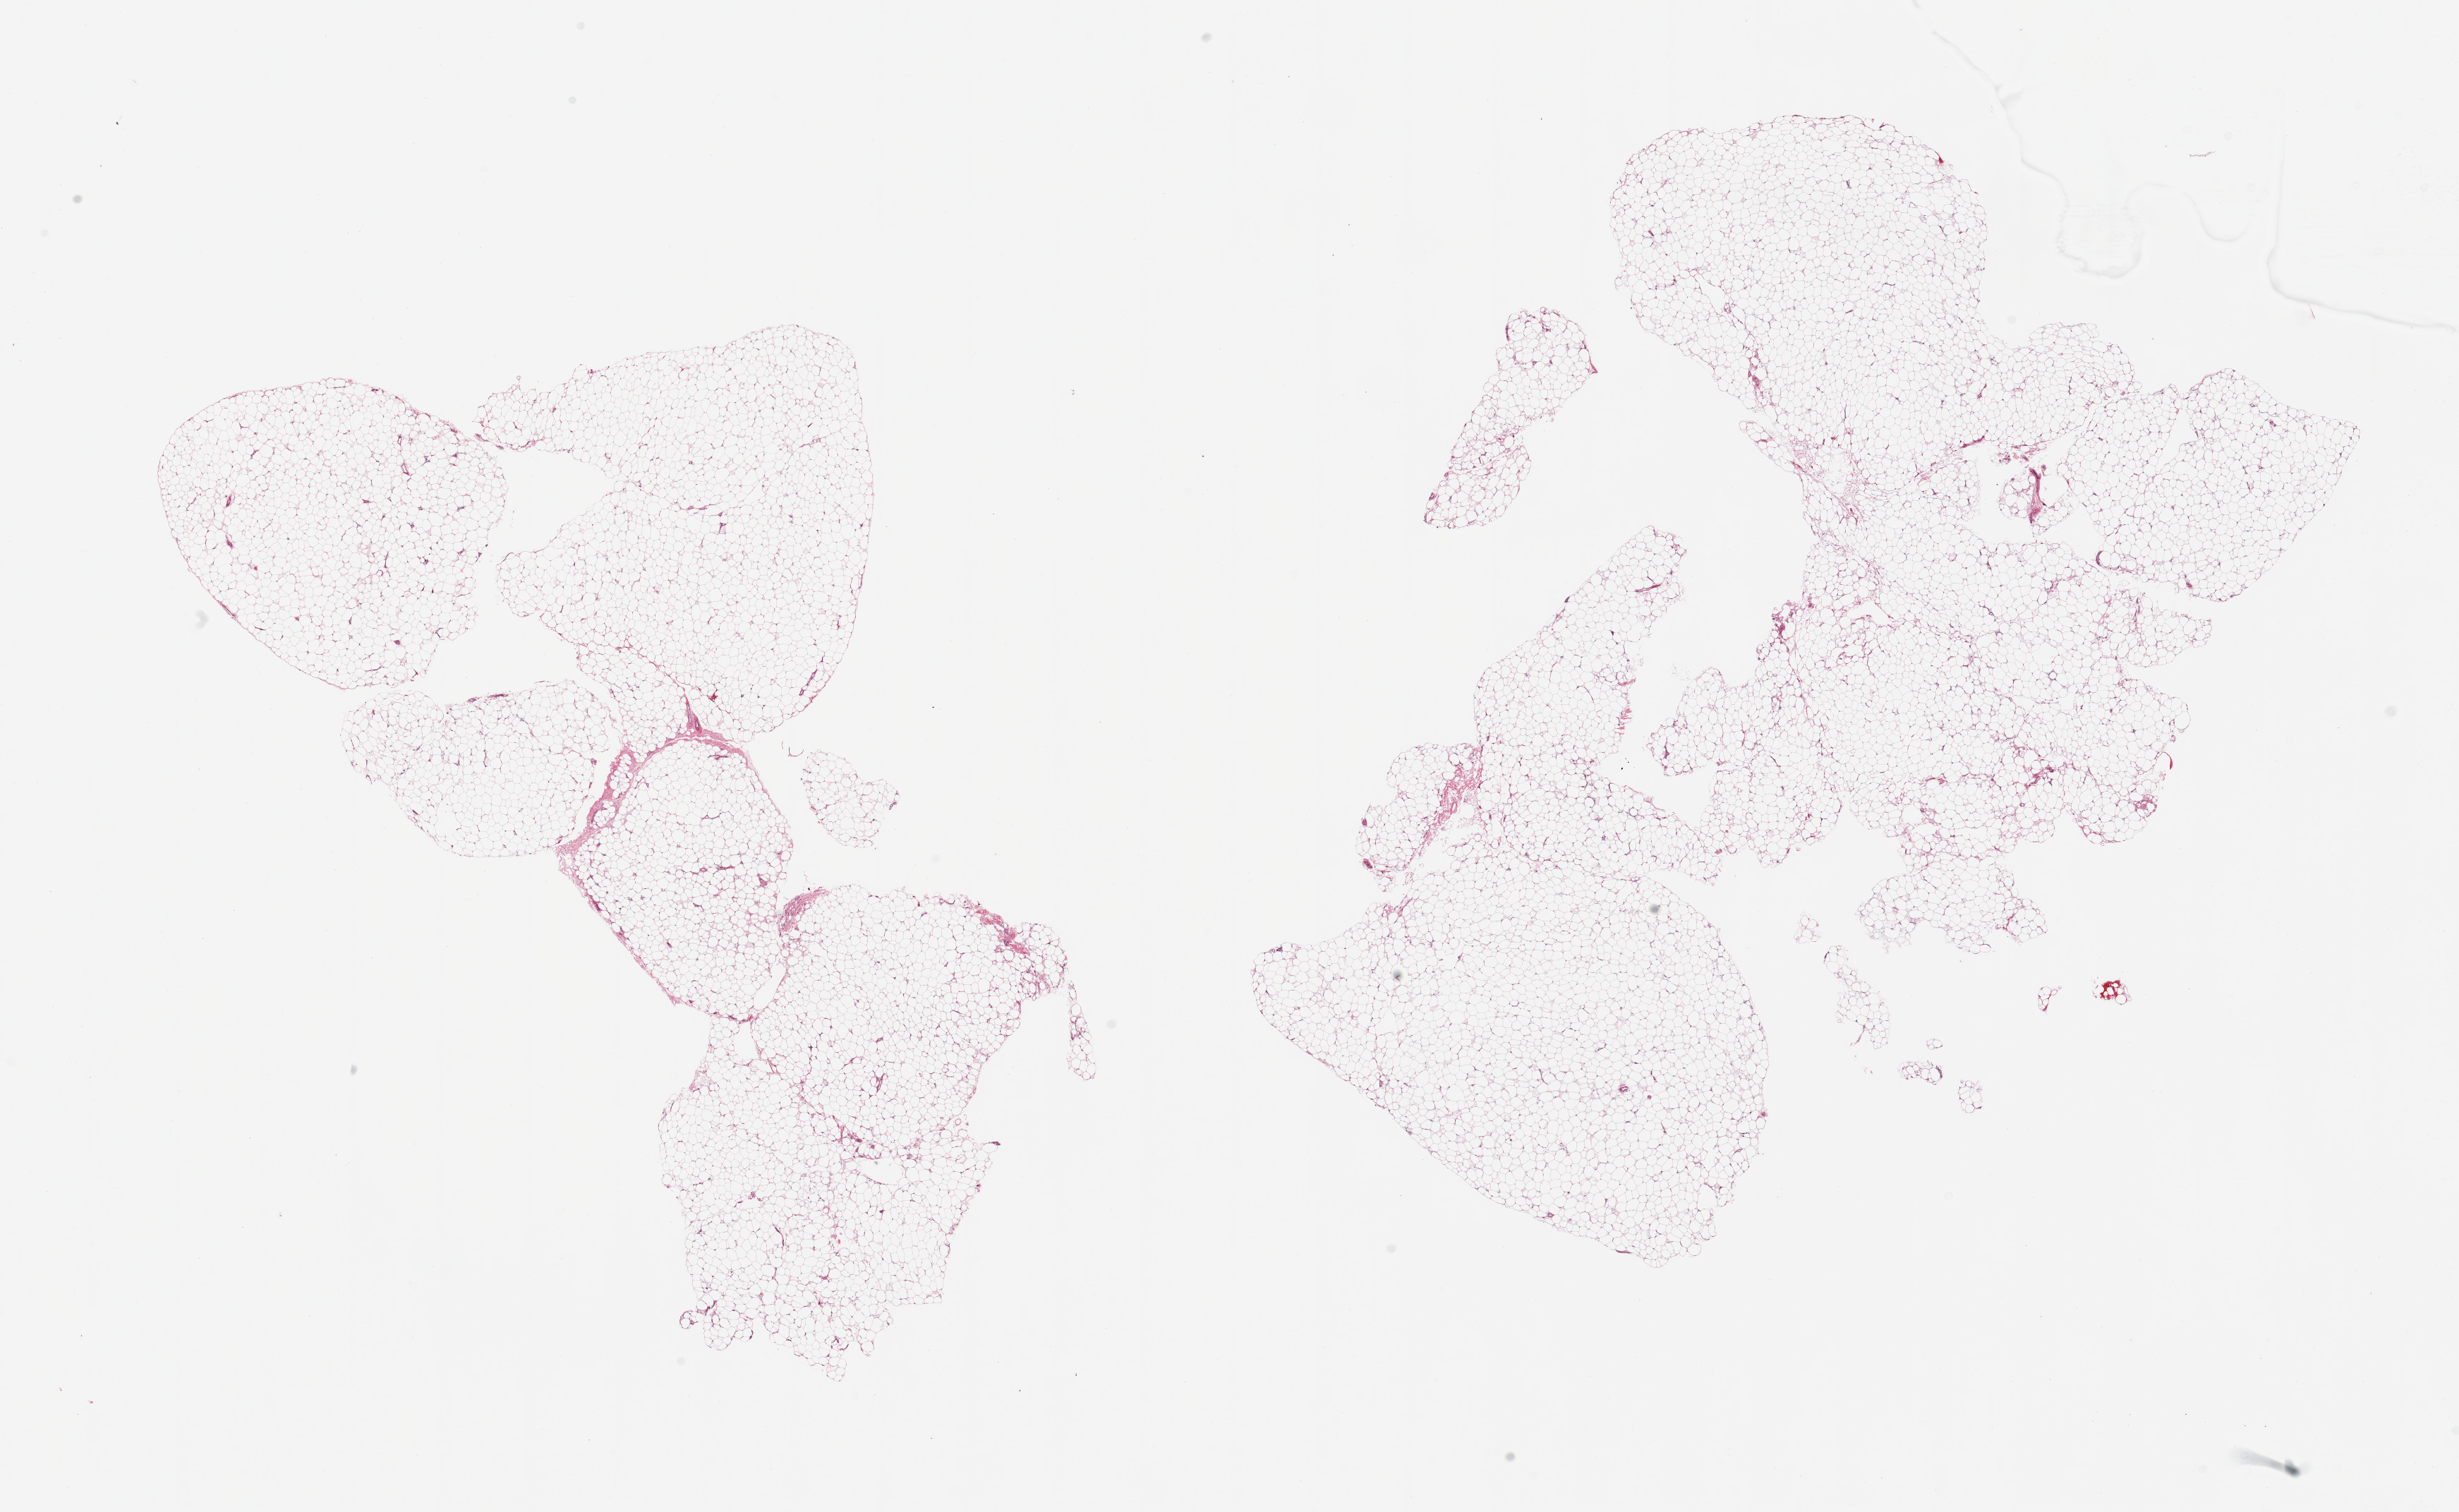
Whole-slide image, hematoxylin and eosin (H&E) stain — shown as a low-resolution overview of the whole scanned area (about 27.6 x 16.9 mm); PAXgene-fixed paraffin-embedded (PFPE) section; section of adipose tissue (target tissue); donor tissue sample. Female donor.
Review note (as recorded): 2 pieces.